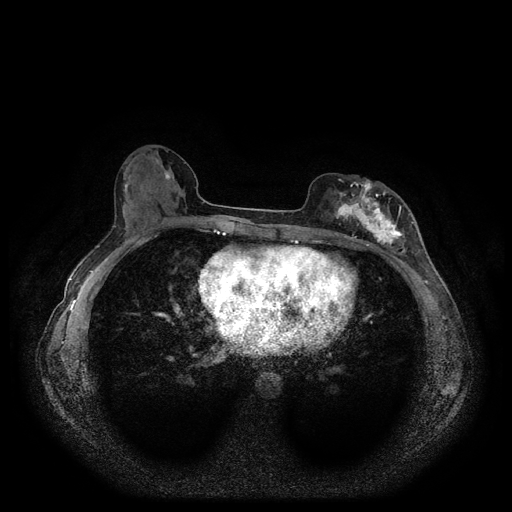
Breast MRI (dynamic contrast-enhanced, multi-phase), one axial slice; slice 49 of 116 in the series (ordered by position); dynamic contrast-enhanced series, time point 2 of 5 at this slice position (early post-contrast); 1.5 T; TE 2.6 ms, TR 5.3 ms; 512 × 512 image matrix. Patient: female, 51 years.
Annotated regions visible in this slice (semi-automatic segmentation, software-assisted and operator-edited):
- breast lesion (labelled 'tumour' in the annotation; benign lesions carry a separate 'benign' label): bounding box [x1, y1, x2, y2] px = [330, 177, 410, 252]
- breast lesion (labelled benign in the annotation): [161, 165, 172, 181]